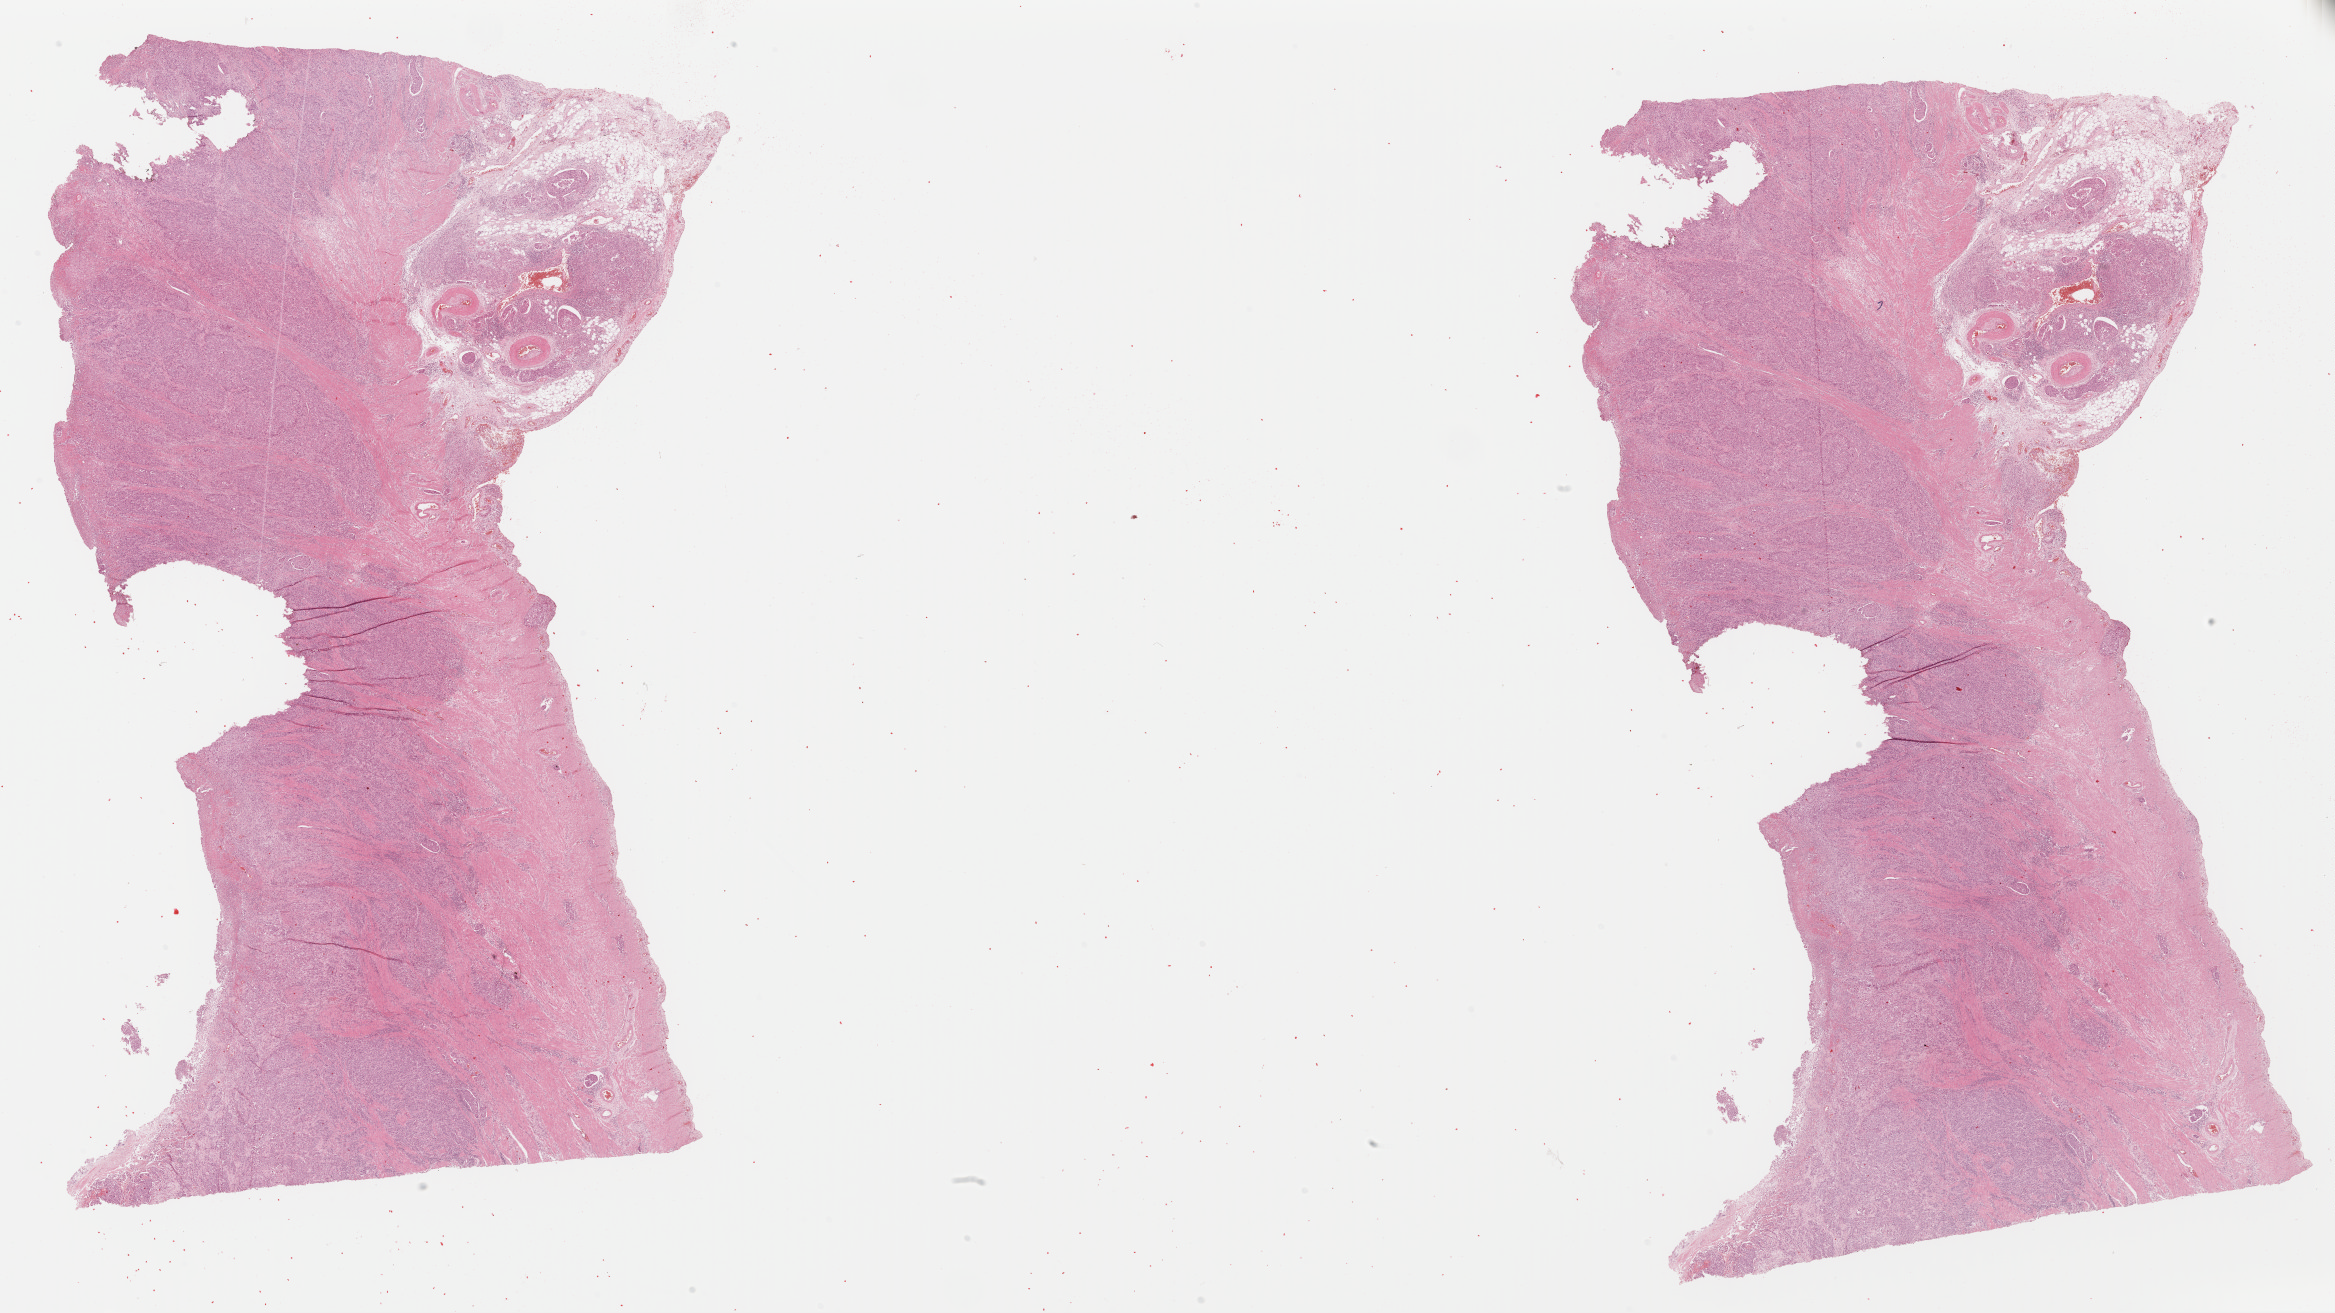
H&E-stained whole-slide image, shown as a low-resolution overview of the whole scanned area (about 36.7 x 20.6 mm, from a 40x scan); formalin-fixed paraffin-embedded (FFPE) diagnostic section; primary tumour sample from the stomach. Male, age 53 years at initial diagnosis. Histologic grade: G3 (poorly differentiated).
• pathologic diagnosis: Tubular adenocarcinoma (gastric antrum)
• AJCC pathologic stage: IIIA